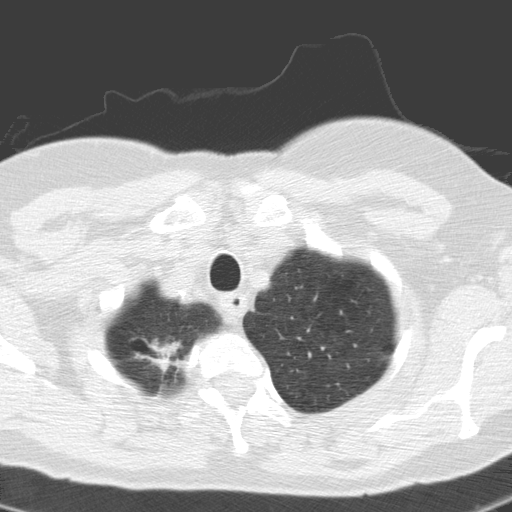
Low-dose screening chest CT, axial slice. Baseline screening round. Lung window (W 1500 / L -600 HU). 3.2 mm slice thickness. Slice 12 of 155 in the series. 512 × 512 image matrix. Female participant, aged 60 years at enrolment. Current smoker at enrolment.
Lesion marked by an expert reader, bounding box [x1, y1, x2, y2] px = [117, 323, 197, 393]. No non-calcified nodule or mass ≥4 mm was recorded by the screening reader at this exam.